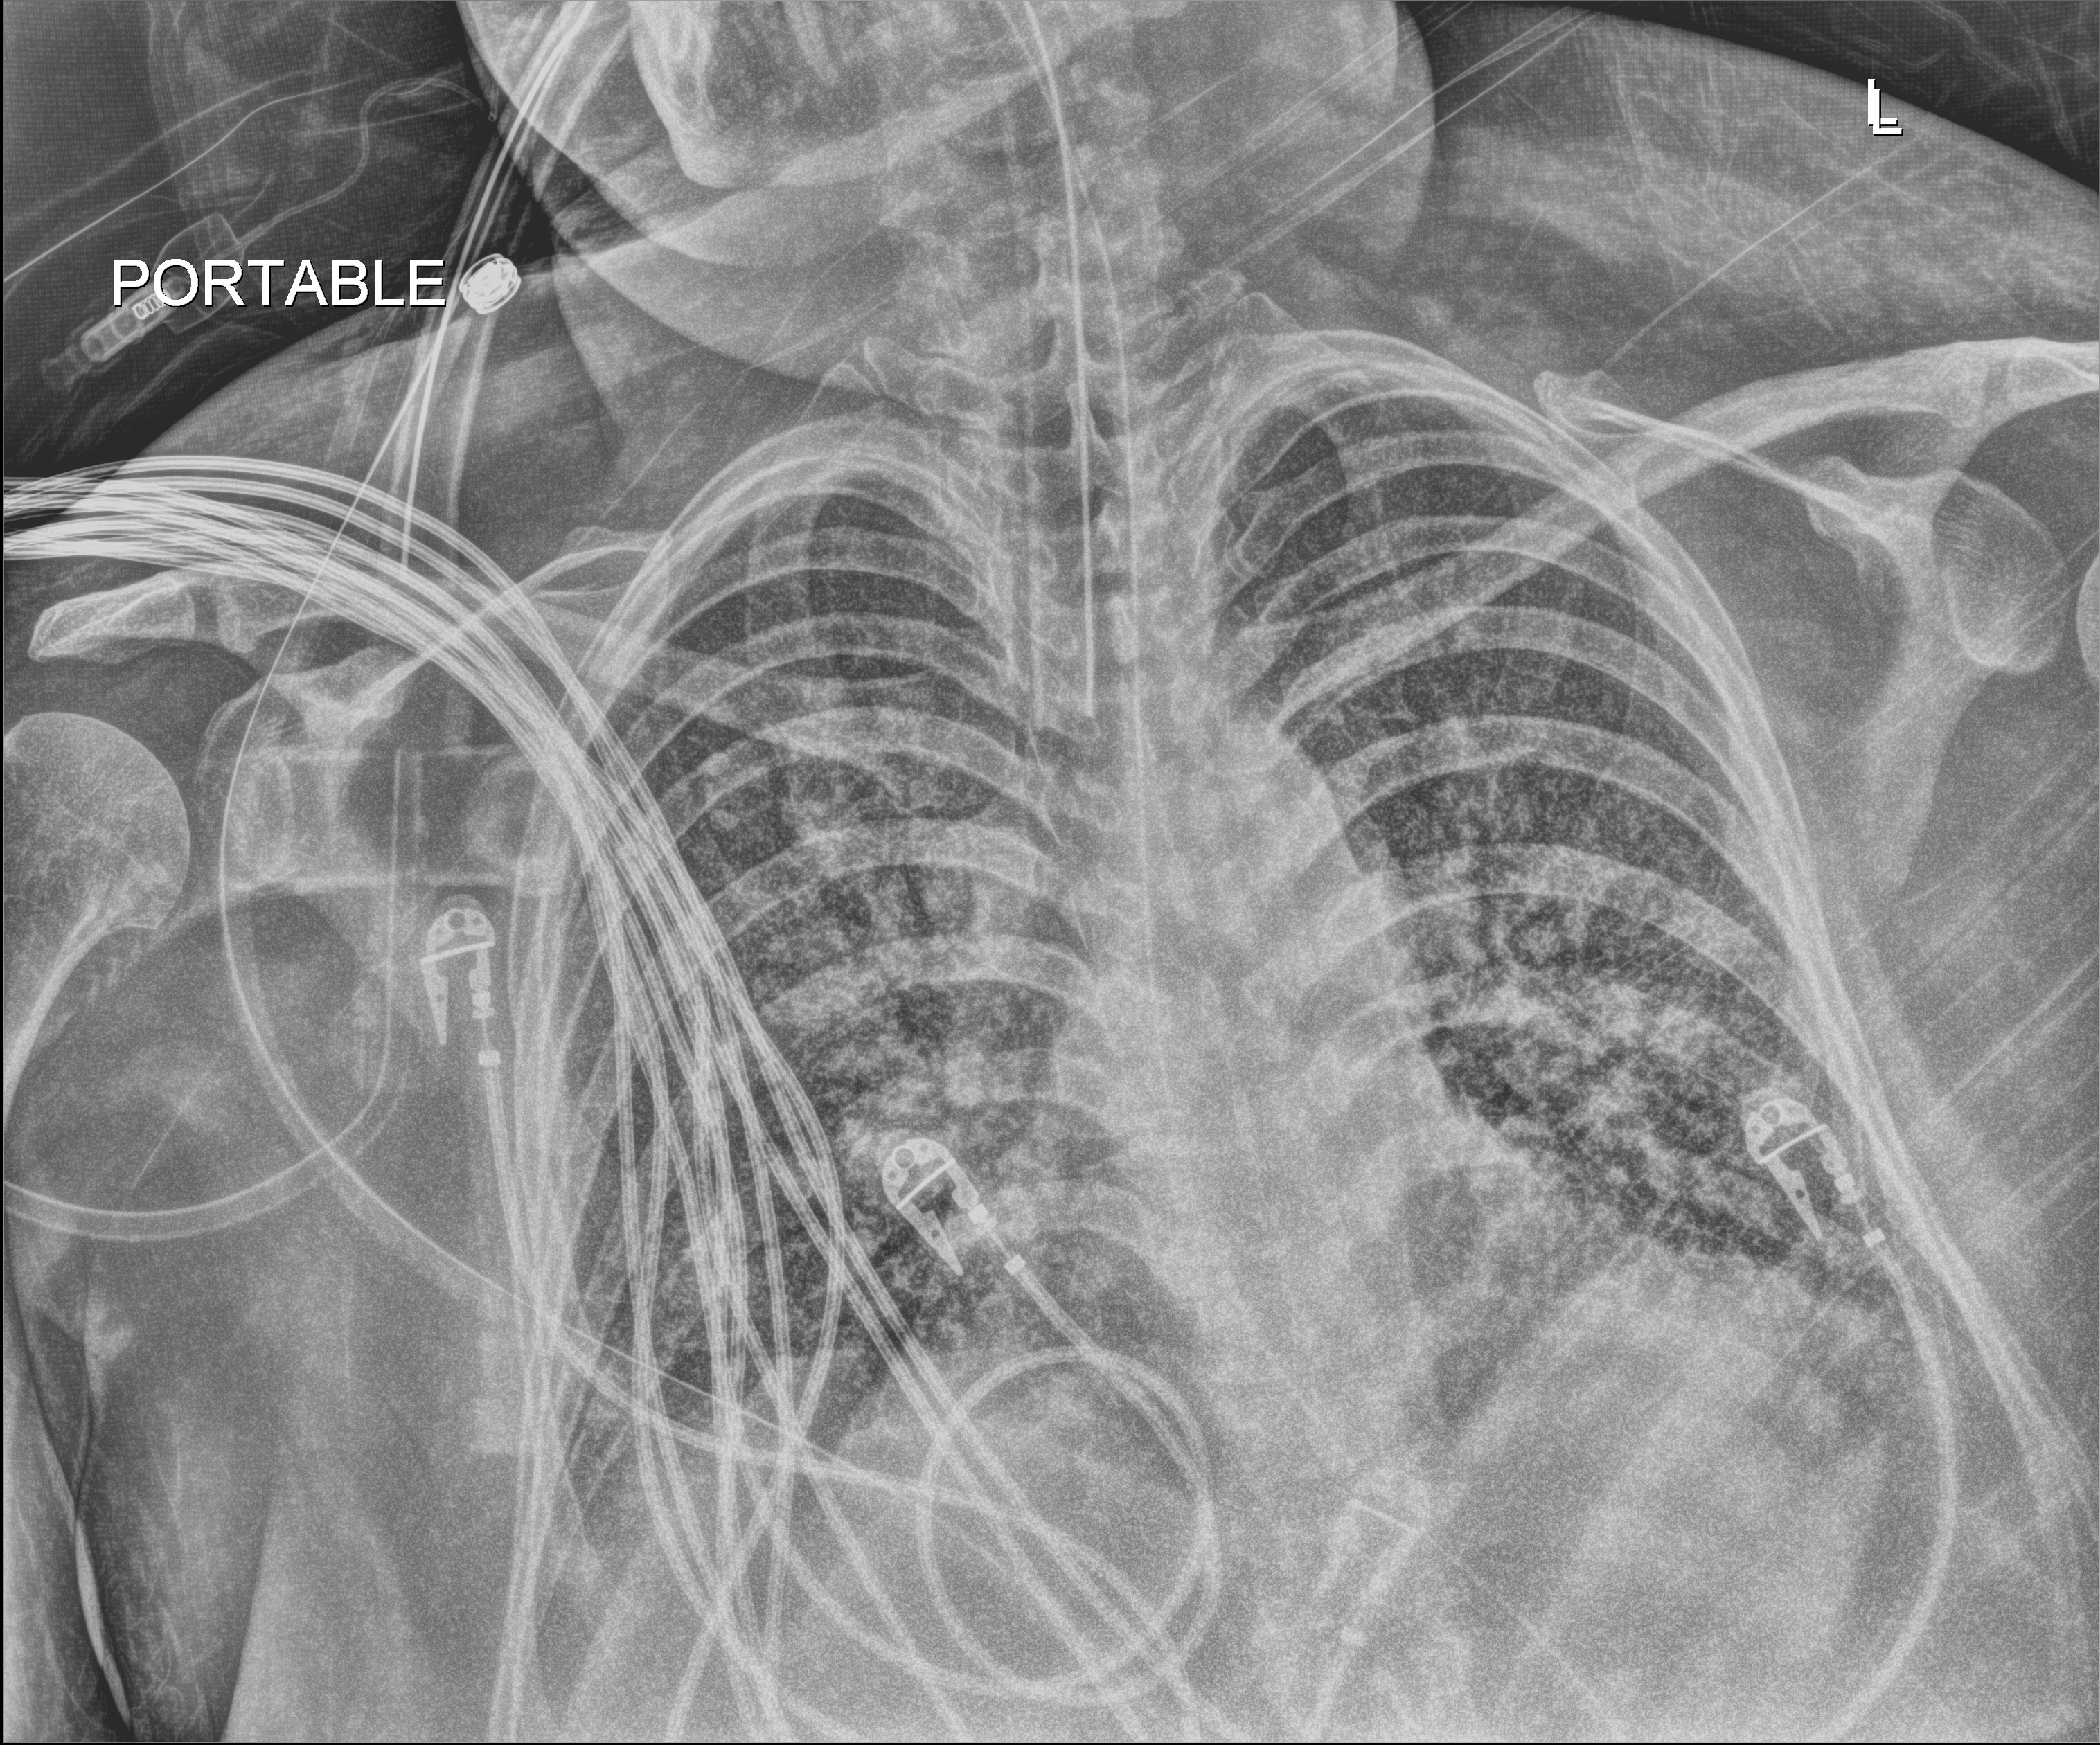
Bedside chest radiograph (digital radiography). Patient hospitalised with COVID-19, aged 18–59 years.
From the hospital-stay record, not from the radiograph (when in the stay this image was taken is not recorded):
- smoking status (admission record): never
- mechanically ventilated during this hospital stay: yes